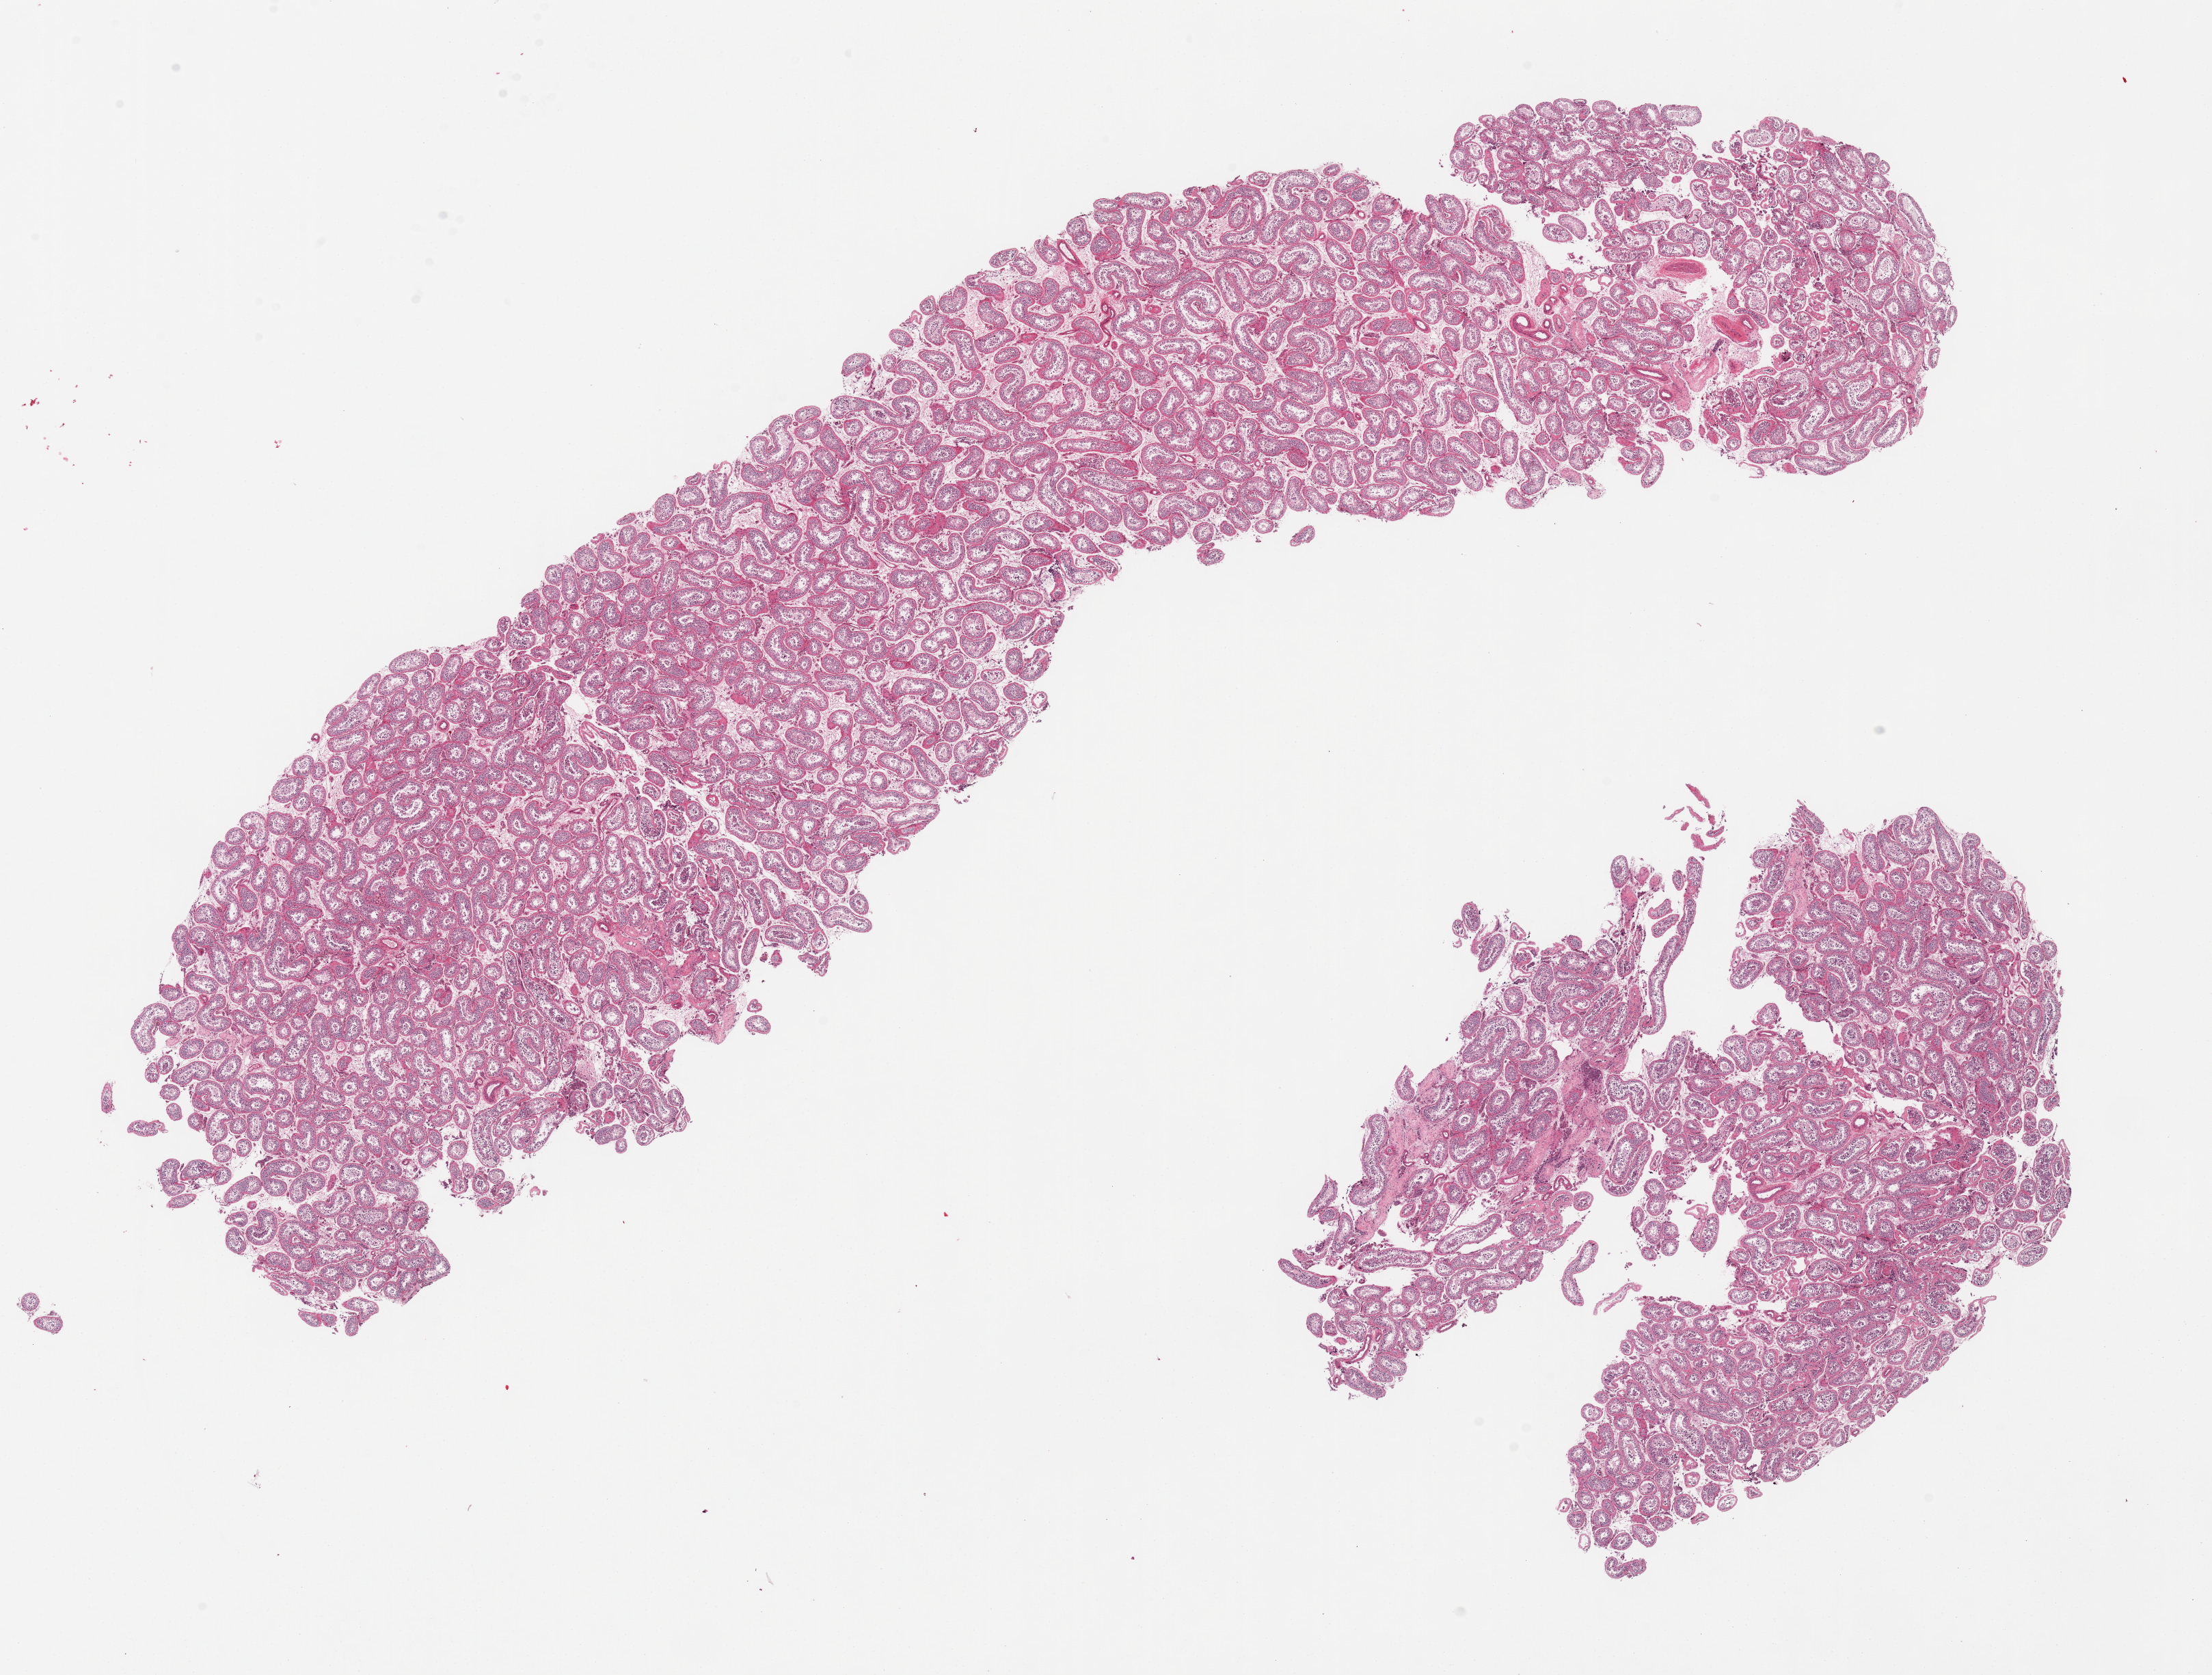
Digitized haematoxylin and eosin-stained section, a low-resolution overview of the entire scanned area, about 25.6 x 19.4 mm; PAXgene-fixed paraffin-embedded (PFPE) section; target tissue: testis; donor tissue sample. Donor: male.
Reviewer comment on this tissue sample: 2 pieces, spermatogenesis.